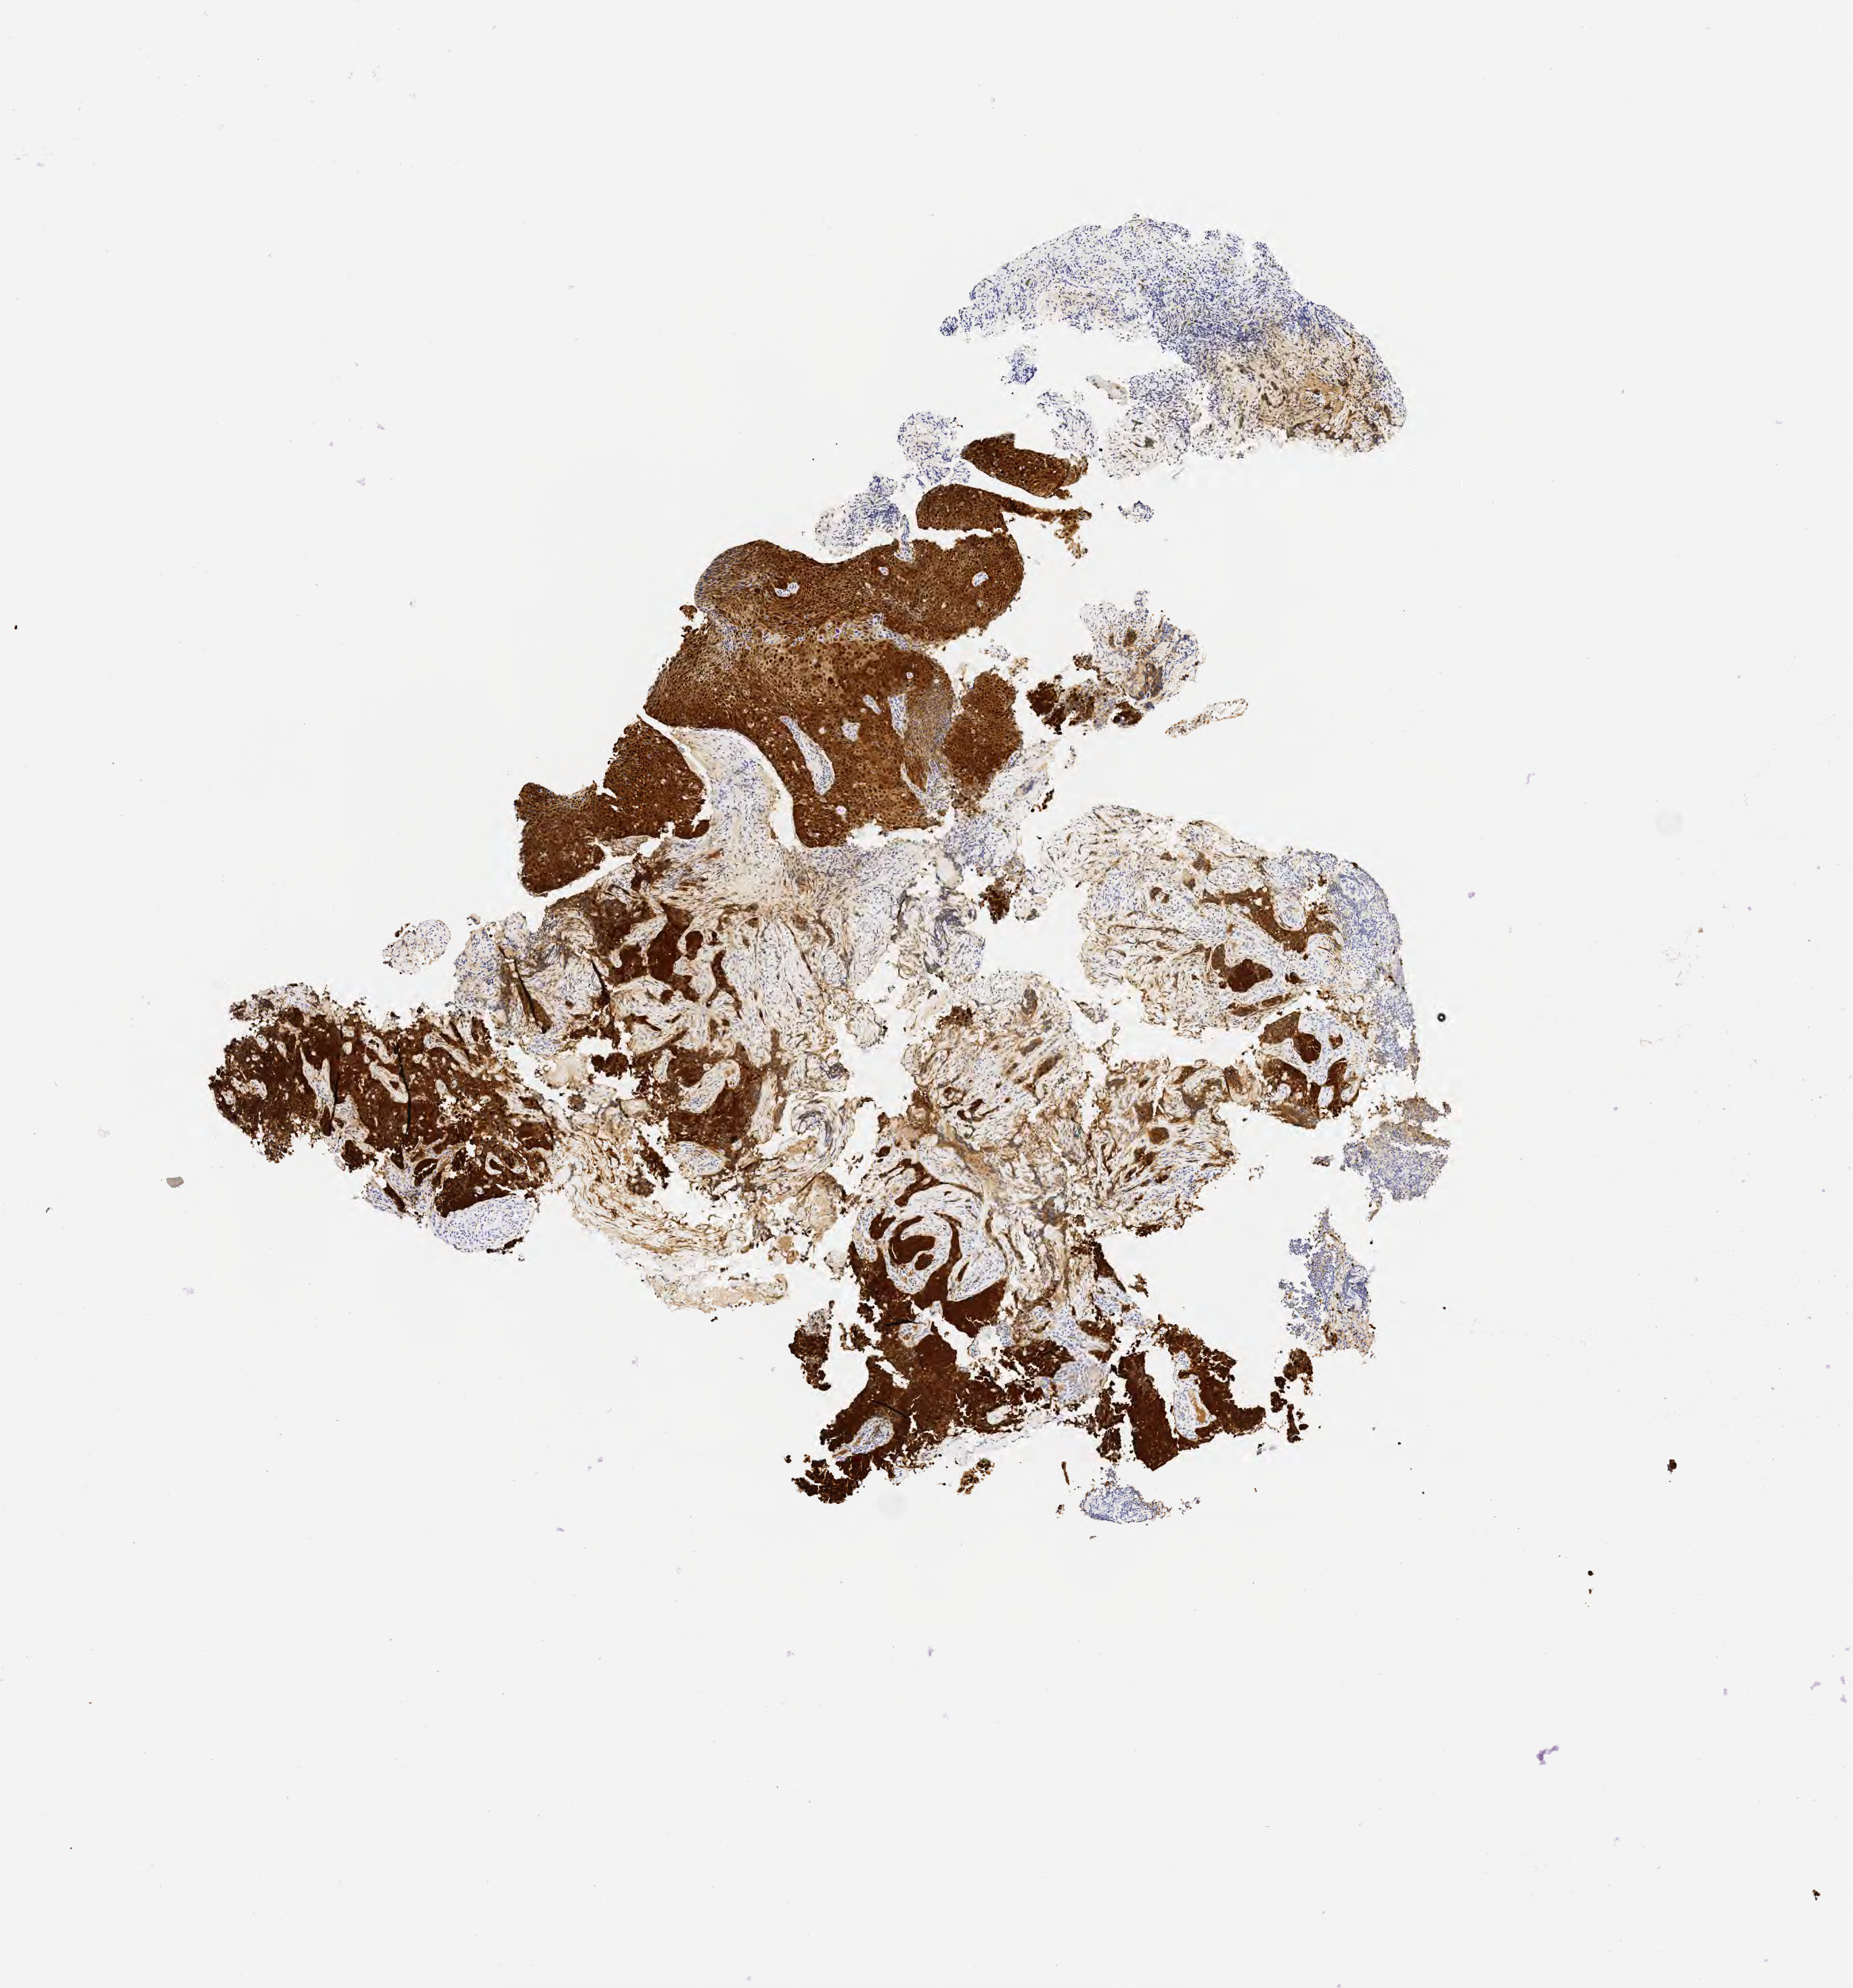
IHC for p16 (p16INK4a), whole-slide image — whole scanned area (about 5.5 x 5.9 mm) shown as a low-resolution overview; tumor tissue; anatomic site: cervix. Patient female; aged 30.
- diagnosis: Squamous cell carcinoma, large cell, nonkeratinizing, NOS